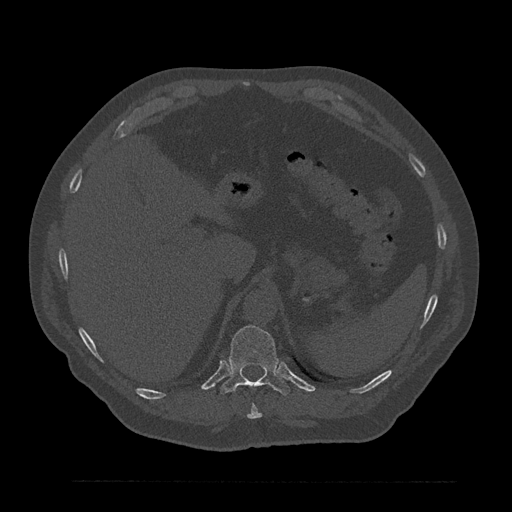
CT including the spine, one axial slice. Position 306 of 797 along the scan axis. Reconstruction kernel Br40s/3. 120 kVp. Bone window (W 1800 / L 400 HU). 0.5 mm slice thickness. 512 × 512 image matrix, field of view 430 × 430 mm. Male patient, age 61 years. From the clinical record (not read from this slice): primary cancer: prostate.
Structures marked on this image (semi-automatic segmentation, software-assisted and operator-edited):
- T10 vertebra: bounding box [x1, y1, x2, y2] px = [247, 405, 262, 419]
- T11 vertebra: [220, 325, 290, 396]